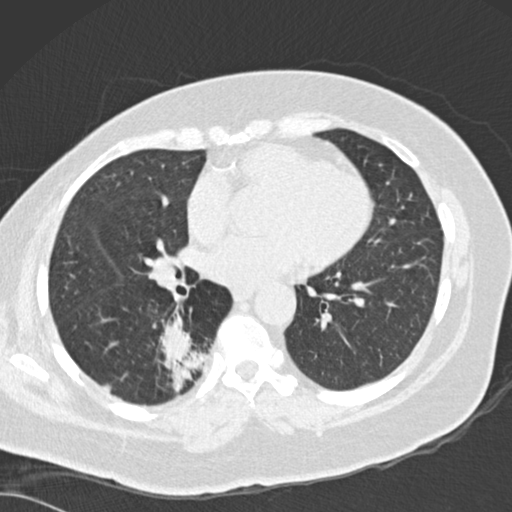
Low-dose screening chest CT, axial slice; first (baseline) screen; lung window (W 1500 / L -600 HU); 2 mm slice thickness; standard (soft-tissue) reconstruction kernel (B30f); 120 kVp; slice 91 of 162 in the series. Female, age 66 years at enrolment. Current smoker at enrolment.
Expert reader's lesion annotation, box from (x=152, y=323) to (x=224, y=396) px. The screening reader recorded 3 non-calcified nodules or masses ≥4 mm on this exam (left lower lobe, left lower lobe, right lower lobe); which of them this box marks is not recorded.